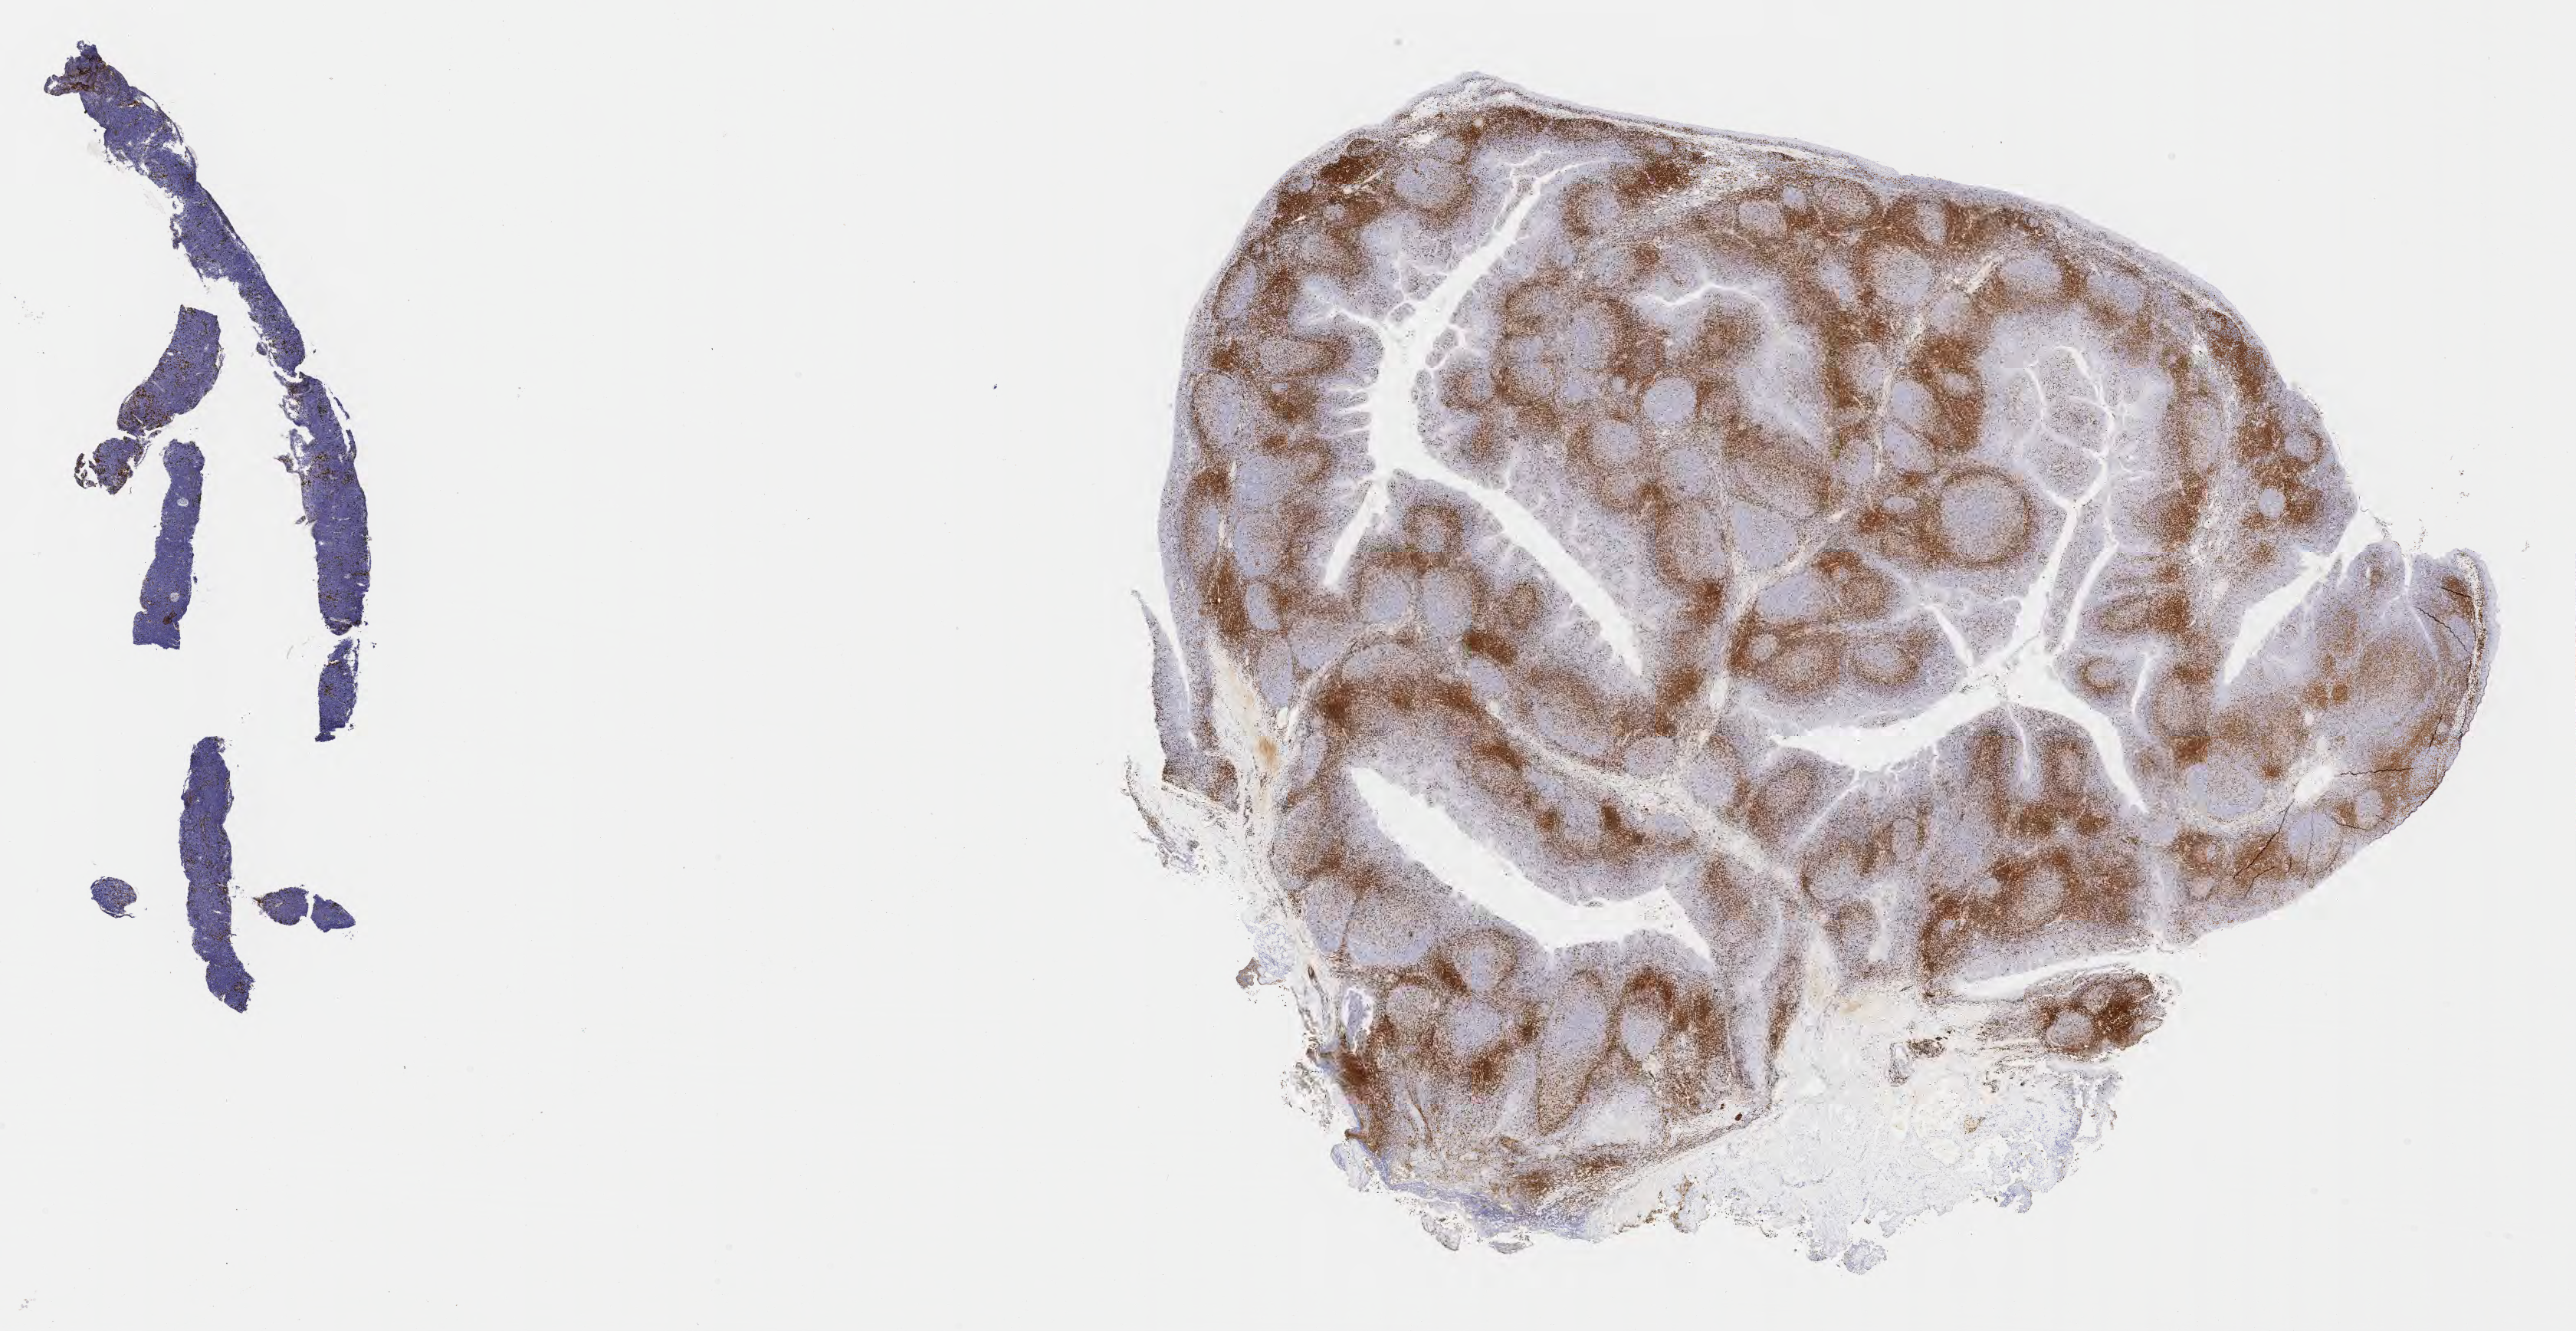
Immunohistochemistry (IHC) whole-slide image stained for CD3 — shown as a low-resolution overview of the whole scanned area (about 27.2 x 14.0 mm); tumor tissue. Male, age 8 years at initial diagnosis.
* histologic diagnosis: Burkitt lymphoma, NOS